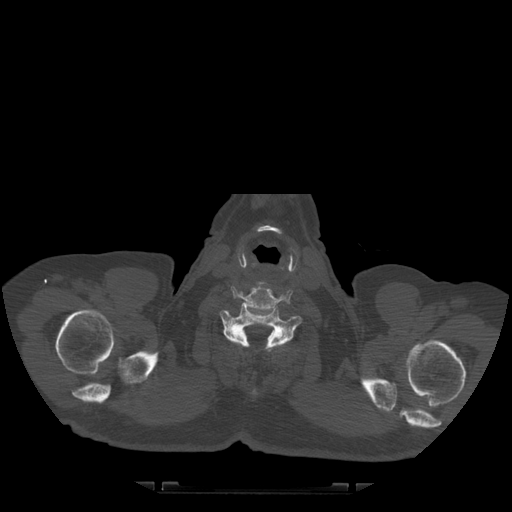
CT including the spine, one axial slice. Position 453 of 522 along the scan axis. Bone window (W 1800 / L 400 HU). 512 × 512 image matrix, field of view 420 × 420 mm. Patient age 72 years. From the clinical record (not read from this slice): primary cancer: prostate.
Structures marked on this image (semi-automatically segmented with operator editing):
- T1 vertebra: bounding box (x1, y1, x2, y2) in pixels: (252, 389, 257, 395)